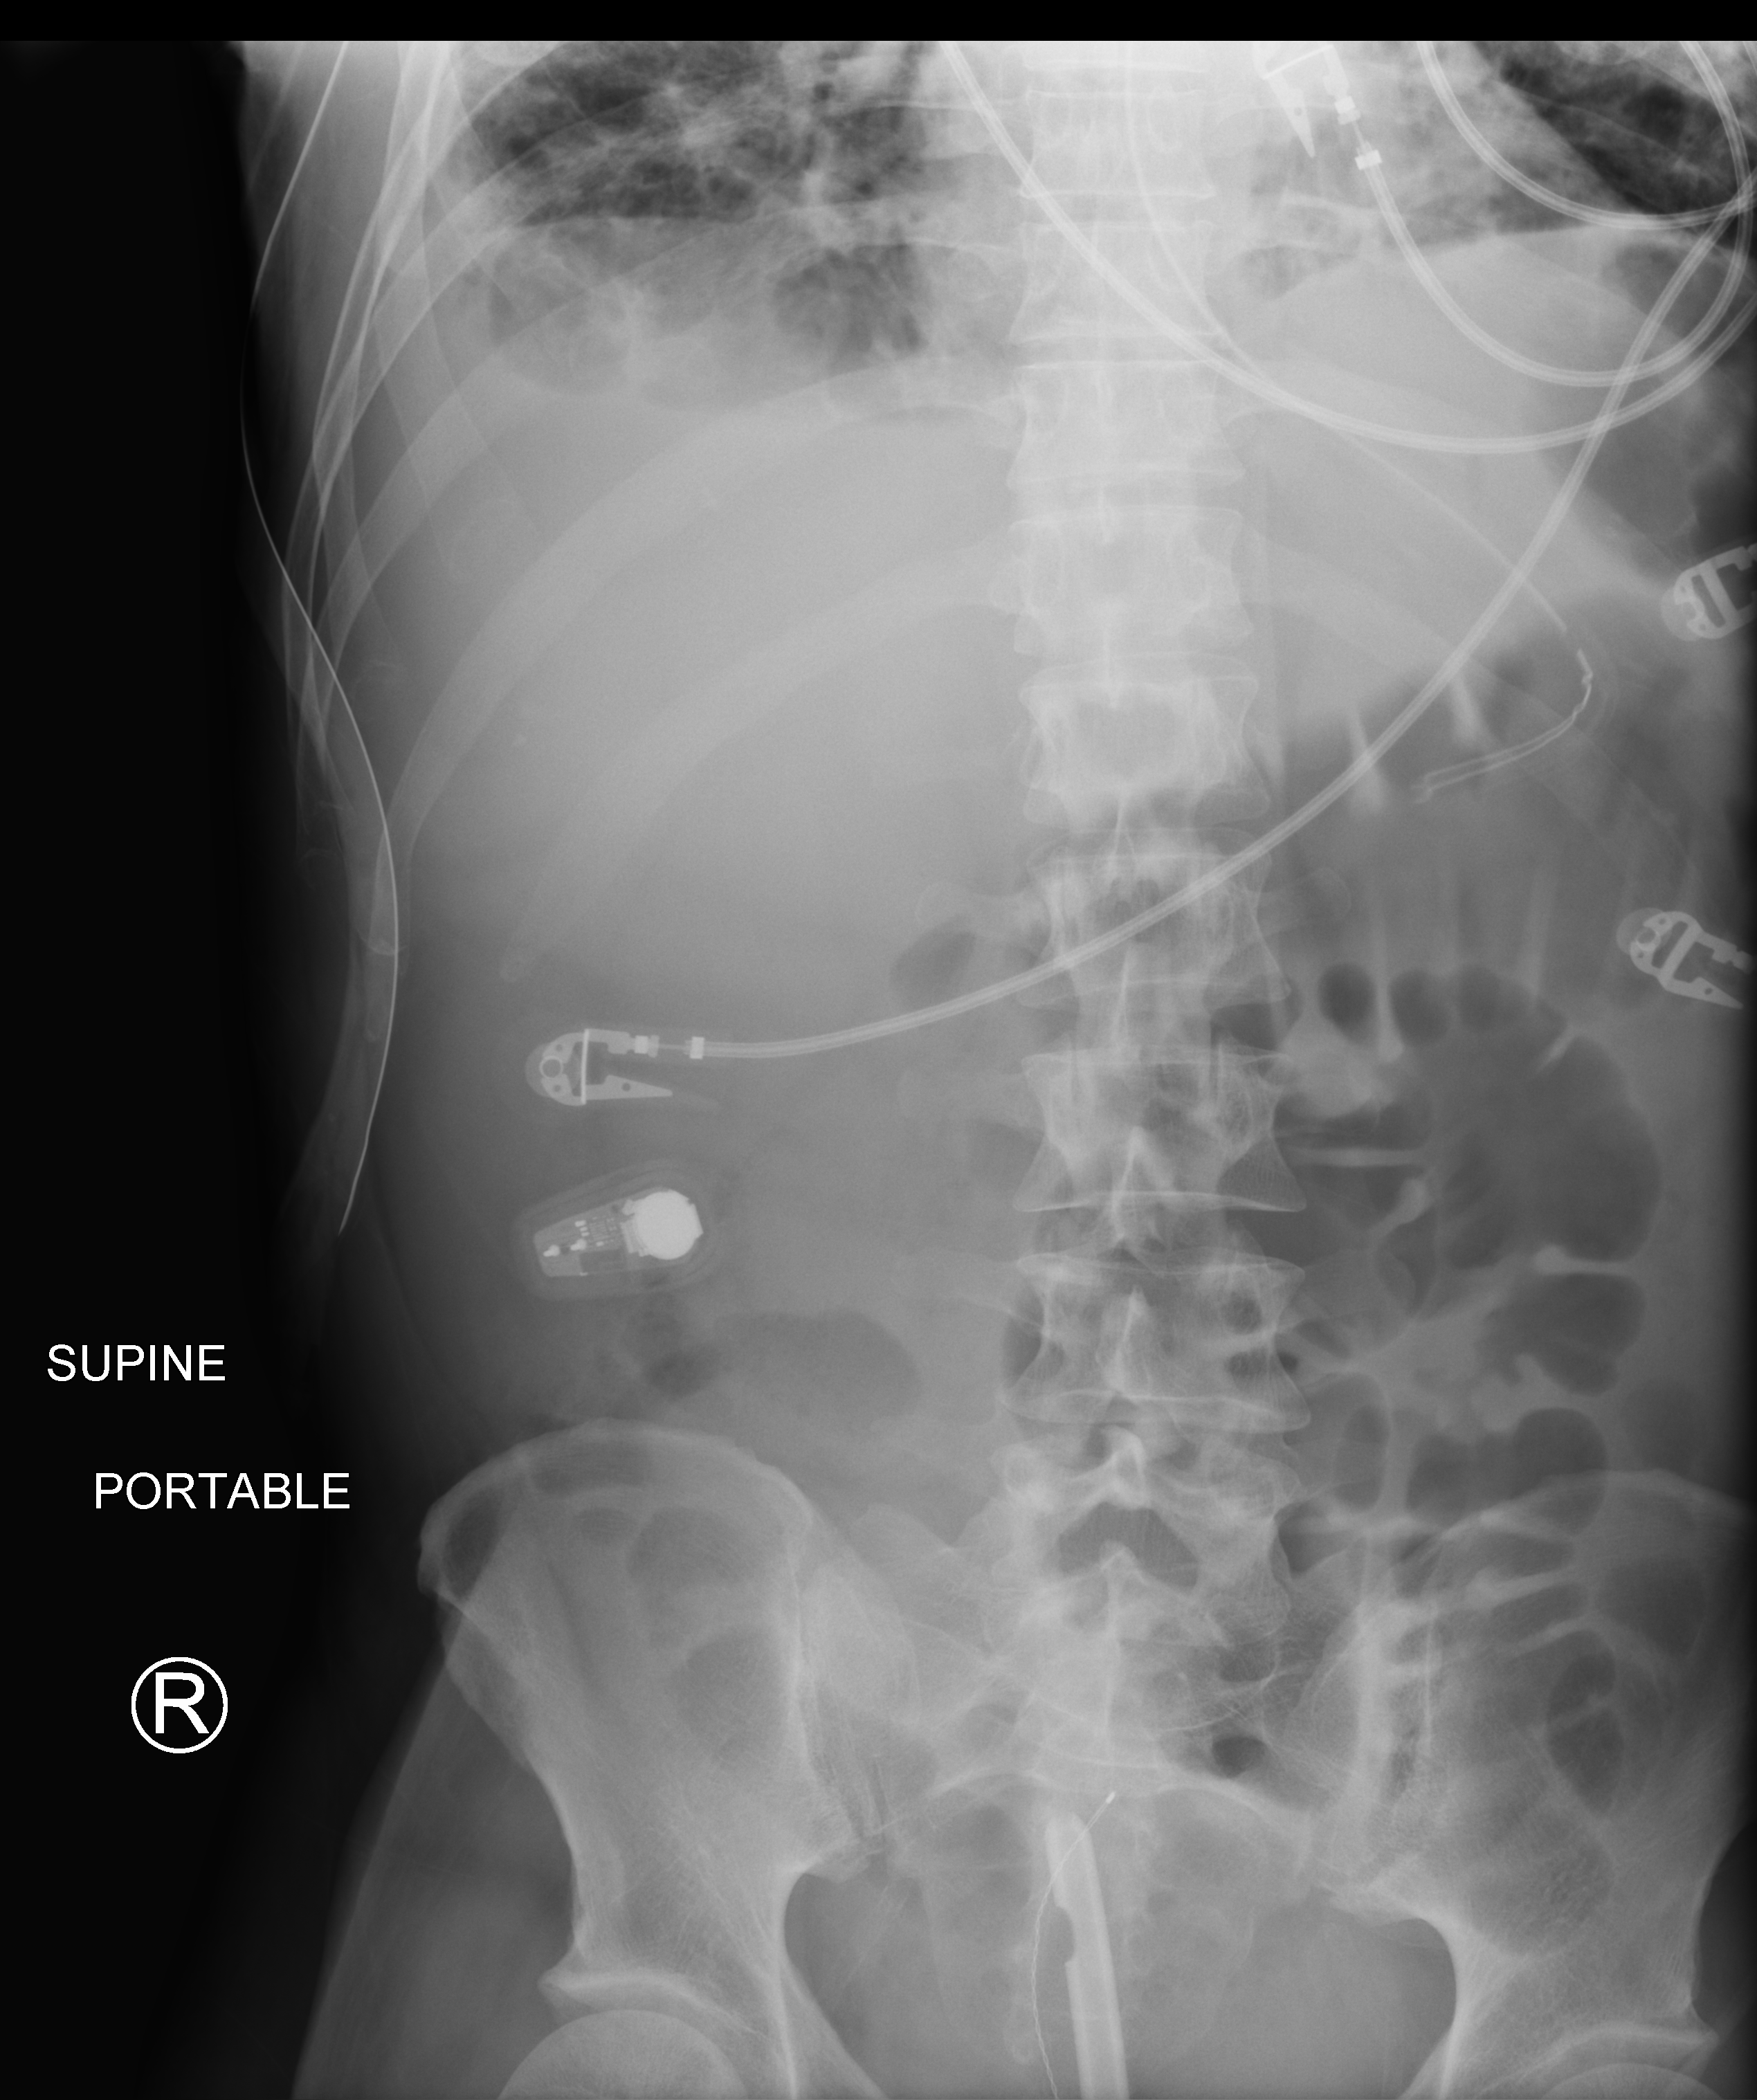
Abdomen X-ray, anteroposterior (AP) projection. Male patient hospitalised with COVID-19, age 18–59 years.
Admission-level facts for this patient (not findings on this image; timing relative to this image not recorded): mechanically ventilated during this hospital stay: yes; admitted to intensive care during this hospital stay: yes; smoking status (admission record): never.